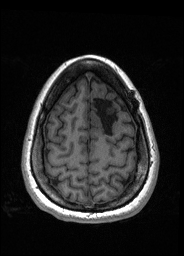
Pre-operative brain MRI before brain-tumour surgery, one axial slice. Position 46 of 176 along the scan axis. T1-weighted post-contrast. 1 mm slice thickness. 184 × 256 image matrix. From the clinical record (not read from this slice): histopathology: Oligodendroglioma; WHO grade: 2; IDH mutation: yes; tumour location: Left Frontal.
Annotated regions visible in this slice (manually delineated by an expert):
- tumour: bounding box (x1, y1, x2, y2) in pixels: (90, 106, 115, 125)